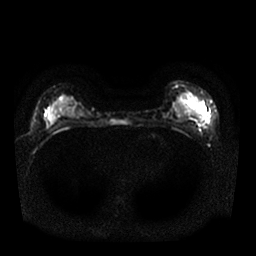
Breast MRI, one axial slice; position 11 of 25 along the scan axis; diffusion-weighted series; image 2 of 4 stored at this slice position (different b-values; order by instance number); 1.5 T; 4 mm slice thickness; 256 × 256 image matrix, field of view 340 × 340 mm. Female patient.
Outlined on this slice (manually delineated by an expert):
- tumour on diffusion-weighted imaging: bounding box [x1, y1, x2, y2] px = [202, 112, 208, 118]